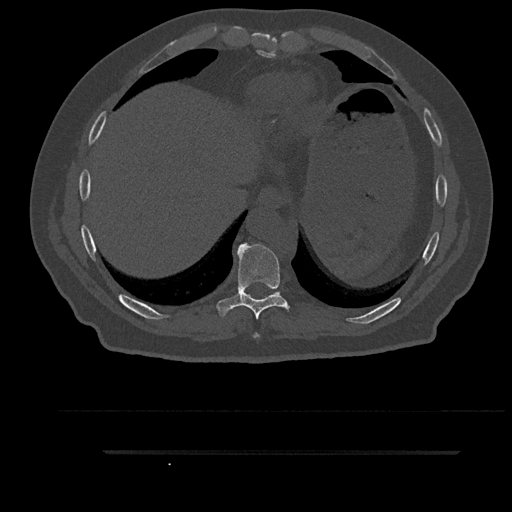
CT including the spine, one axial slice; slice 423 of 797 in the series (ordered by position); reconstruction kernel Br40s/3; 120 kVp; bone window (W 1800 / L 400 HU); 512 × 512 image matrix, field of view 432 × 432 mm. Male patient, age 63 years. Case-level facts recorded for this patient, not image findings: primary cancer: renal; vertebrae with lytic lesions (as recorded): T8.
Annotated regions visible in this slice (semi-automatic segmentation, software-assisted and operator-edited):
- T8 vertebra: box from (x=254, y=333) to (x=259, y=338) px
- T9 vertebra: (x=216, y=243)–(x=294, y=319)